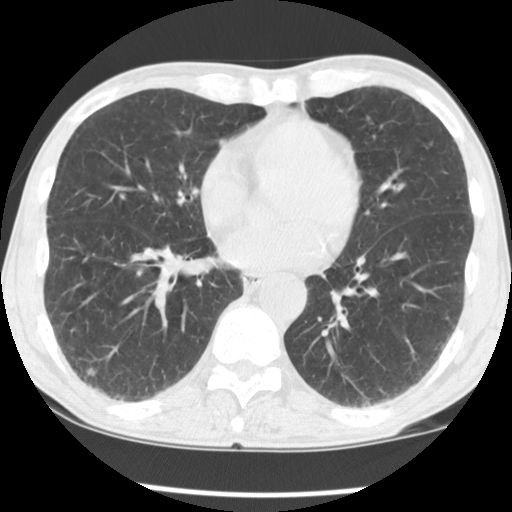
Chest CT (low-dose screening protocol), one axial image. First (baseline) screen. Lung window (W 1500 / L -600 HU). 2.5 mm slice thickness. Standard (soft-tissue) reconstruction kernel (STANDARD). Slice 80 of 135 in the series. 512 × 512 image matrix. Male participant, aged 68 years at enrolment.
Lesion marked by an expert reader, box from (x=66, y=356) to (x=108, y=391) px. The screening reader recorded 4 non-calcified nodules or masses ≥4 mm on this exam (right middle lobe, left upper lobe, right lower lobe, right lower lobe); which of them this box marks is not recorded. Later outcome: lung cancer diagnosed 284 days after this screen — adenocarcinoma, NOS, right lower lobe, moderately differentiated (G2), stage IV (AJCC 6th edition), 14 mm at pathology.